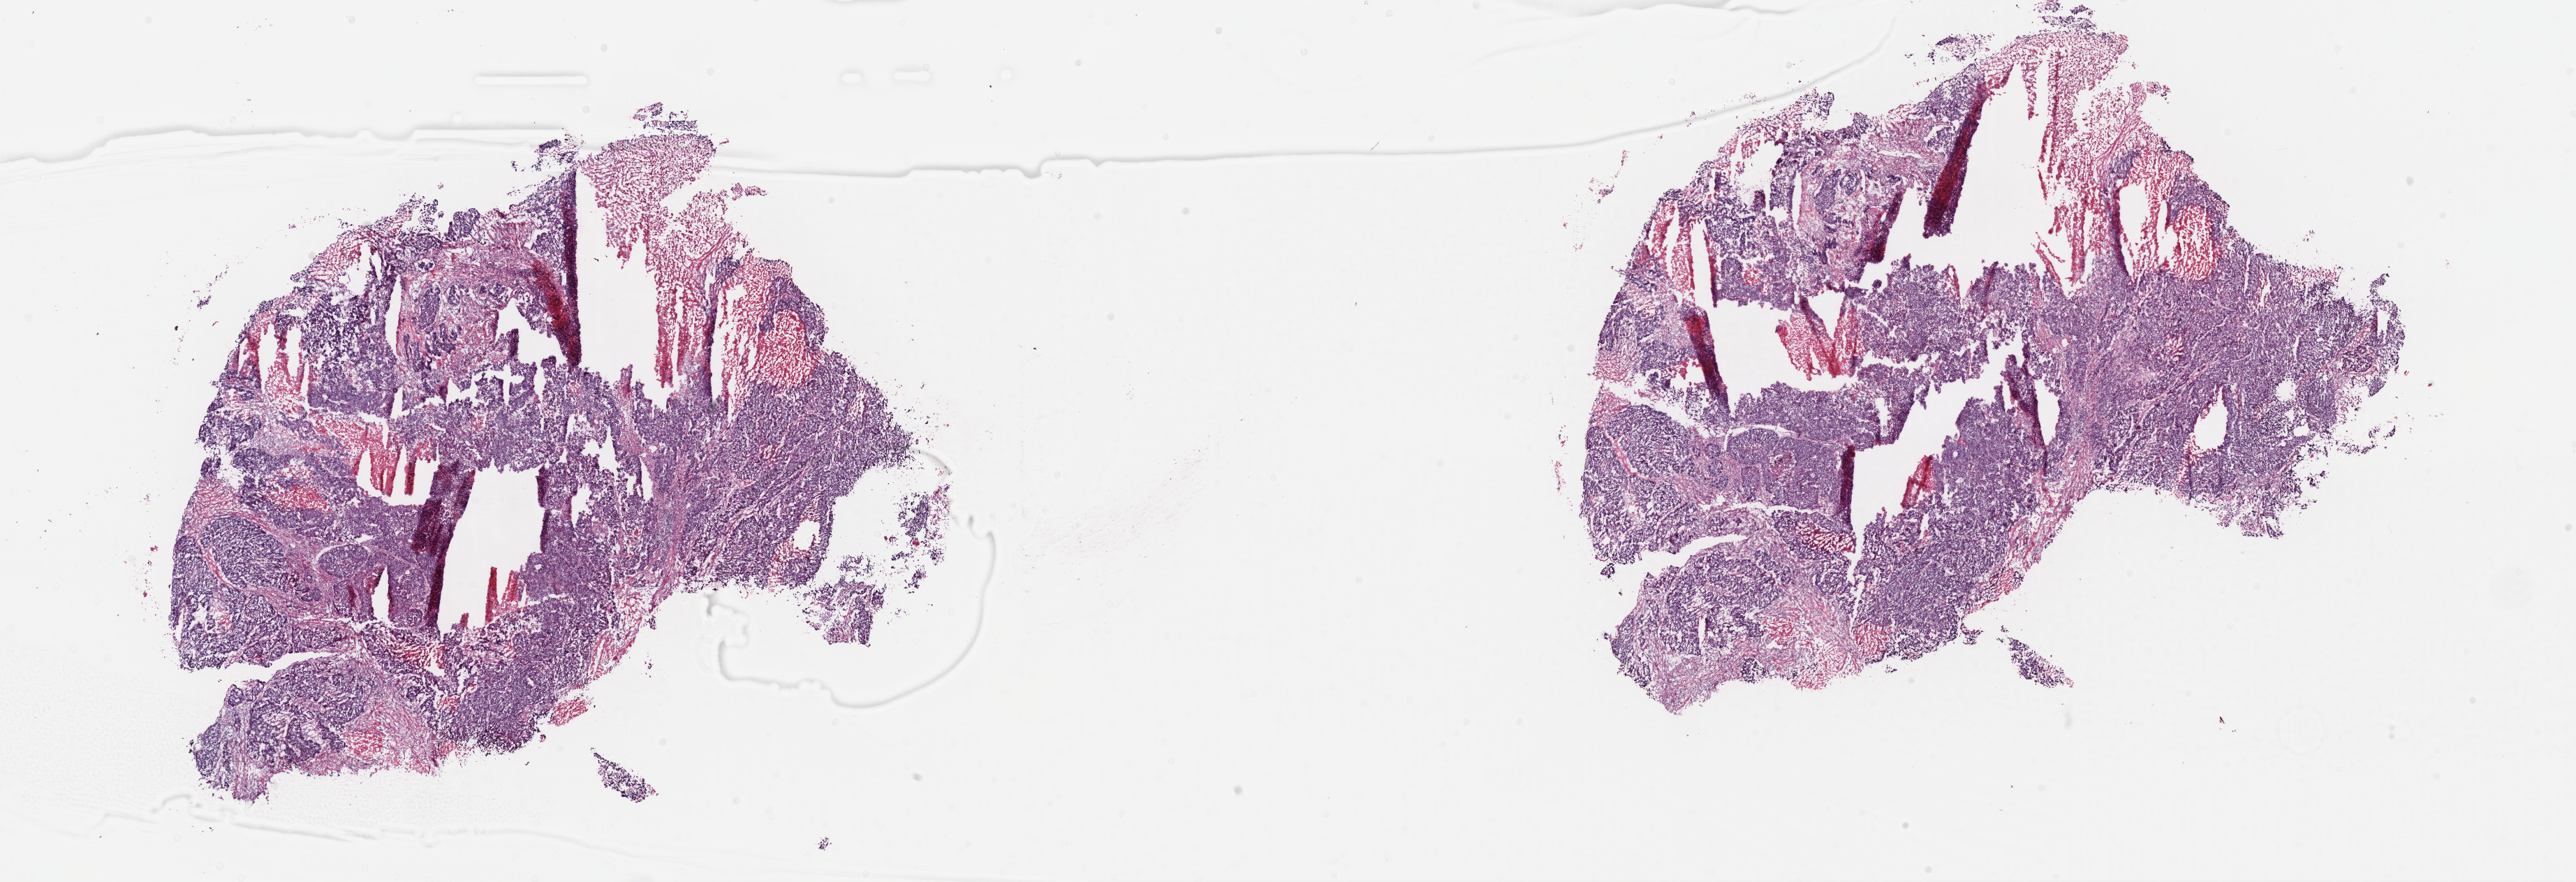
Digitized H&E tissue section (whole slide), shown as a low-resolution overview of the whole scanned area (about 29.1 x 10.0 mm, acquisition: 40x scan); frozen section from the top of the tissue portion; sample: primary tumour, uterus. Female, age 76 years at initial diagnosis. Histologic grade: G3 (poorly differentiated). Composition of this section per pathologist review: tumour cells 75%, tumour nuclei 90%, normal cells 0%, stromal cells 20%, necrosis 5%. Inflammatory infiltration, as recorded: lymphocyte infiltration 5%, monocyte infiltration 3%, neutrophil infiltration 0%.
Pathologic diagnosis: Endometrioid adenocarcinoma, NOS. FIGO stage: IA. Lymph nodes positive (case pathology): 0 of 4 examined.